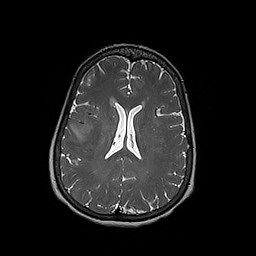
Brain MRI from a brain-tumour surgery series, one axial slice; slice 84 of 192 in the series (ordered by position); 1 mm slice thickness; 256 × 256 image matrix, field of view 250 × 250 mm. From the clinical record (not read from this slice): histopathology: Oligodendroglioma; WHO grade: 3; IDH mutation: yes; tumour location: Right Frontal.
Annotated regions visible in this slice (outlined manually by an expert reader):
- tumour: bounding box (x1, y1, x2, y2) in pixels: (80, 127, 92, 133)